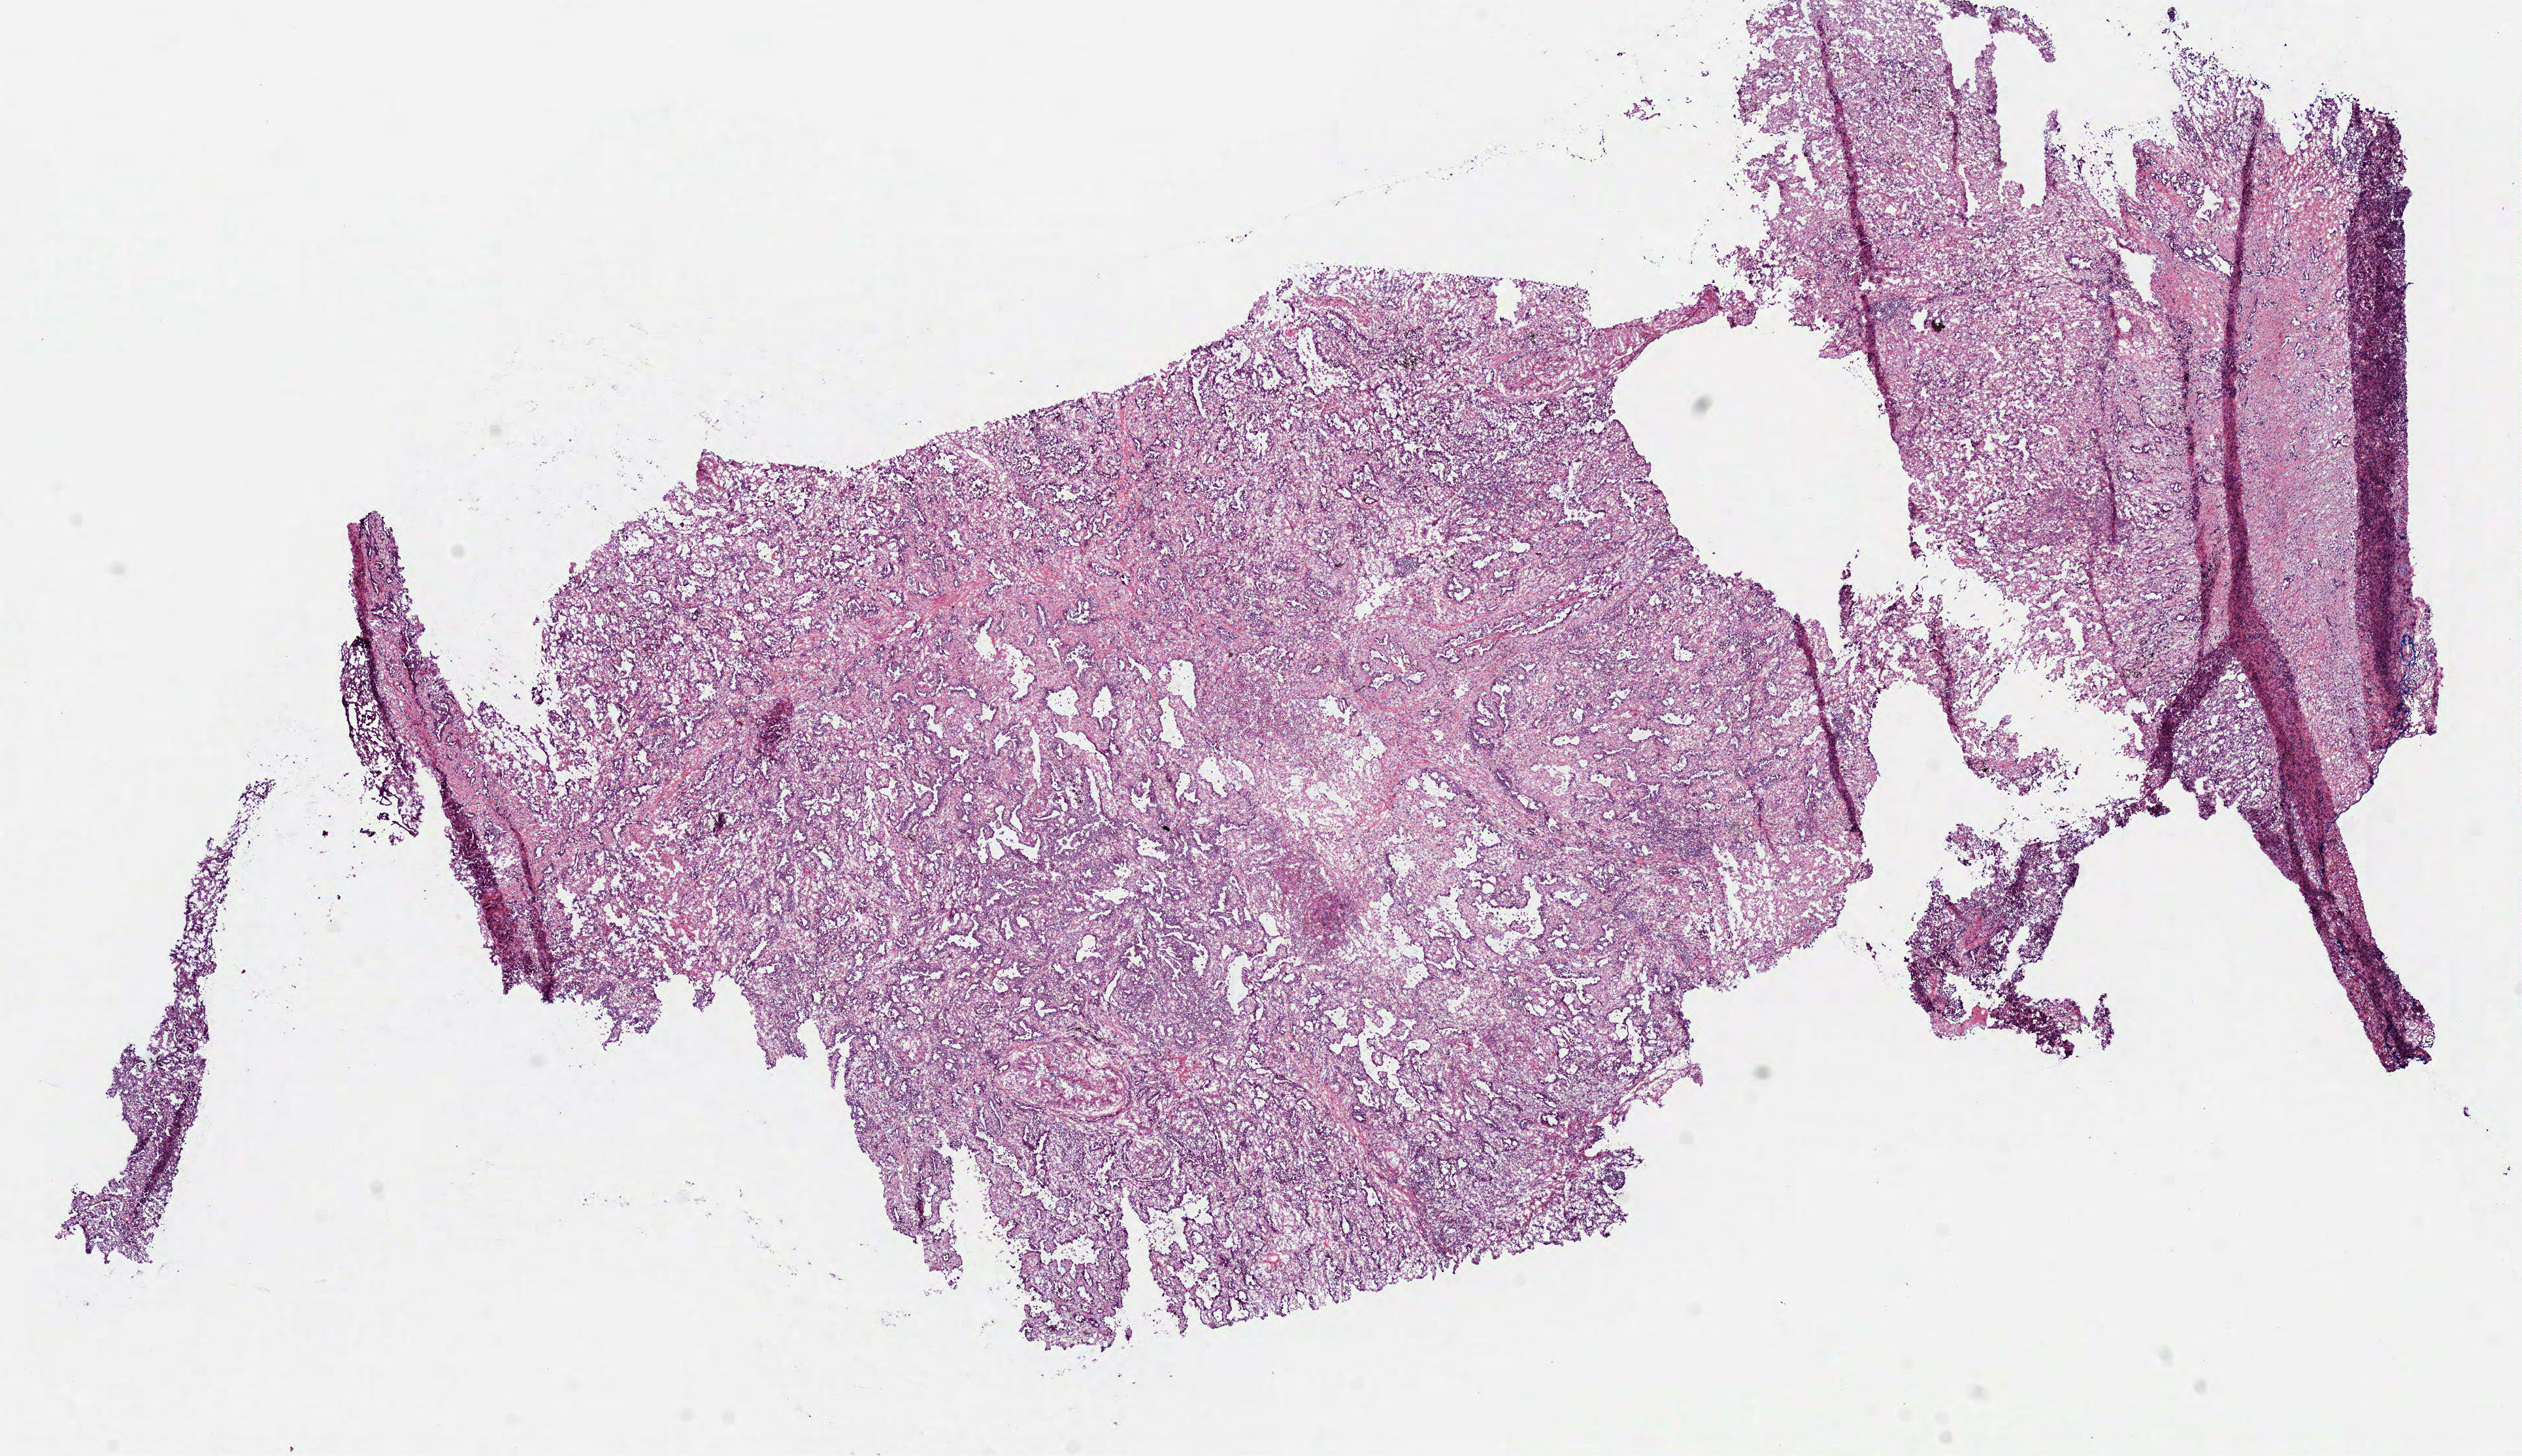
Digitized H&E-stained tissue section (whole slide) — shown as a low-resolution overview of the whole scanned area (about 15.6 x 9.0 mm, acquisition: 40x scan), frozen section from the top of the tissue portion, lung, primary tumour sample. Female, age 70 years at initial diagnosis. Pathologist review of this section (percent, as recorded): tumour cells 50%, tumour nuclei 70%, normal cells 0%, stromal cells 50%, necrosis 0%.
AJCC pathologic stage: IIIA. Laterality: left. Histologic diagnosis: Adenocarcinoma, NOS (upper lobe, lung).